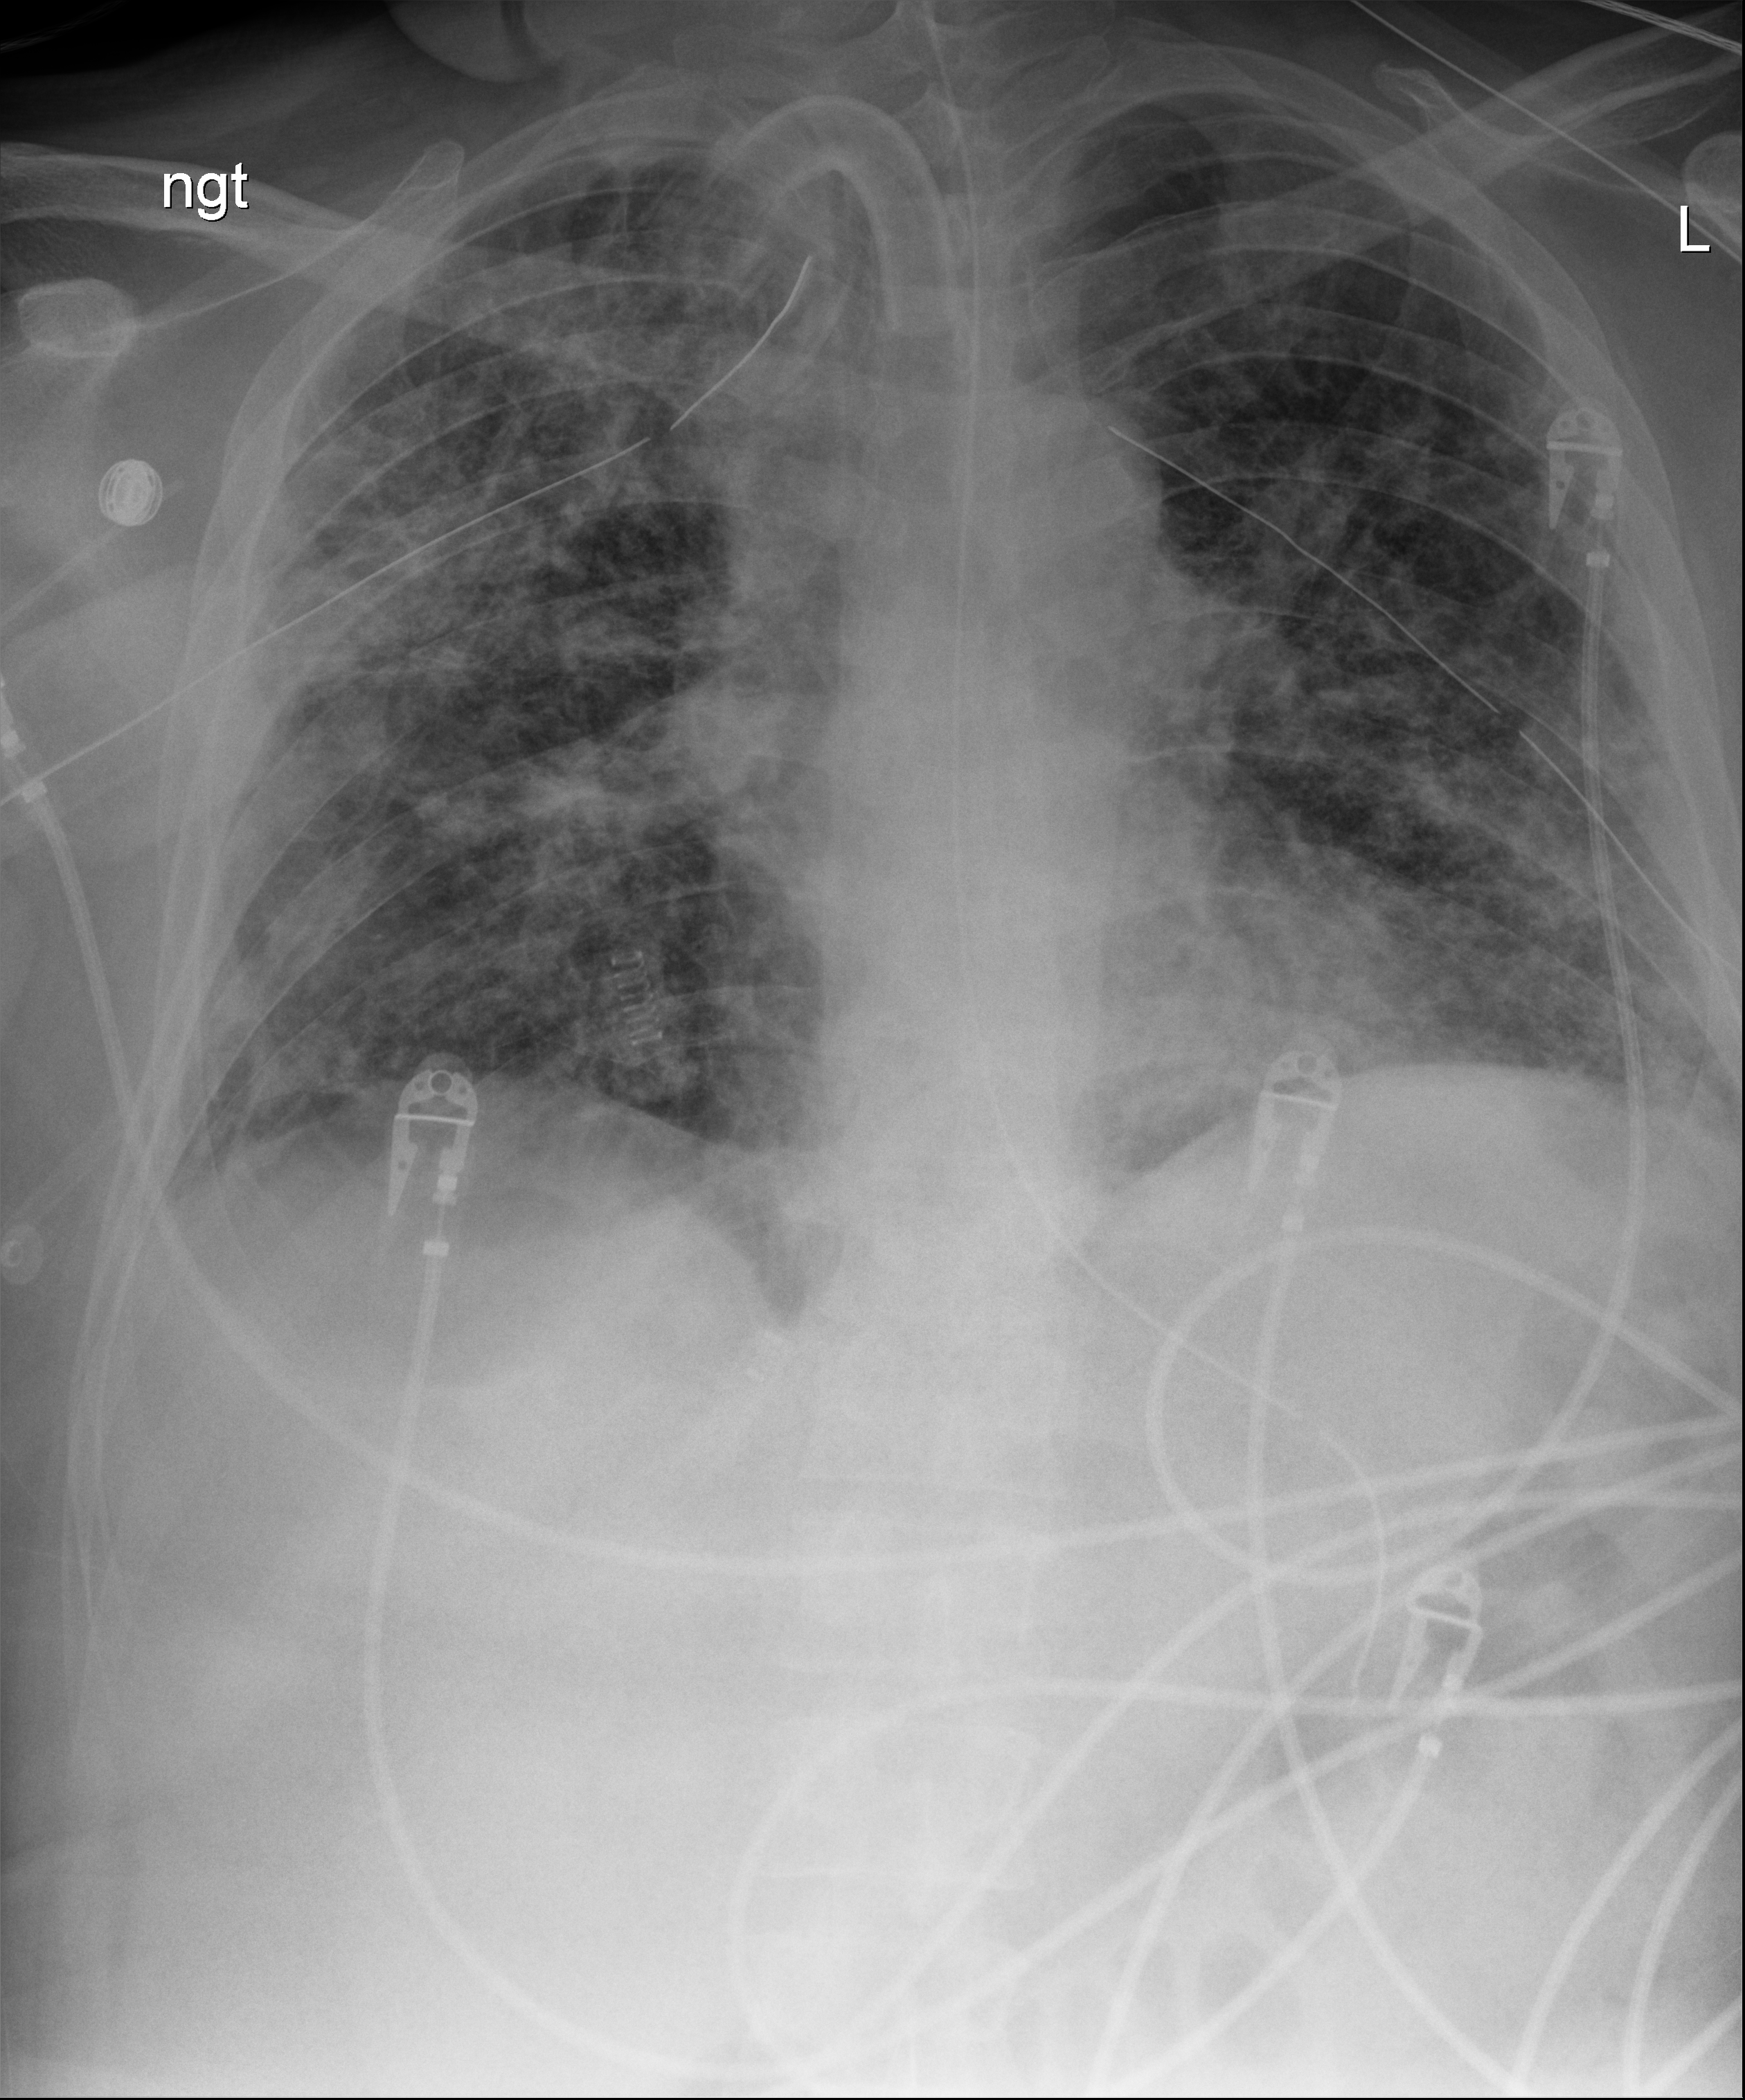
Chest X-ray (portable); anteroposterior (AP) projection. Male patient hospitalised with COVID-19, age 18–59 years.
From the hospital-stay record, not from the radiograph (when in the stay this image was taken is not recorded): admitted to intensive care during this hospital stay: yes.